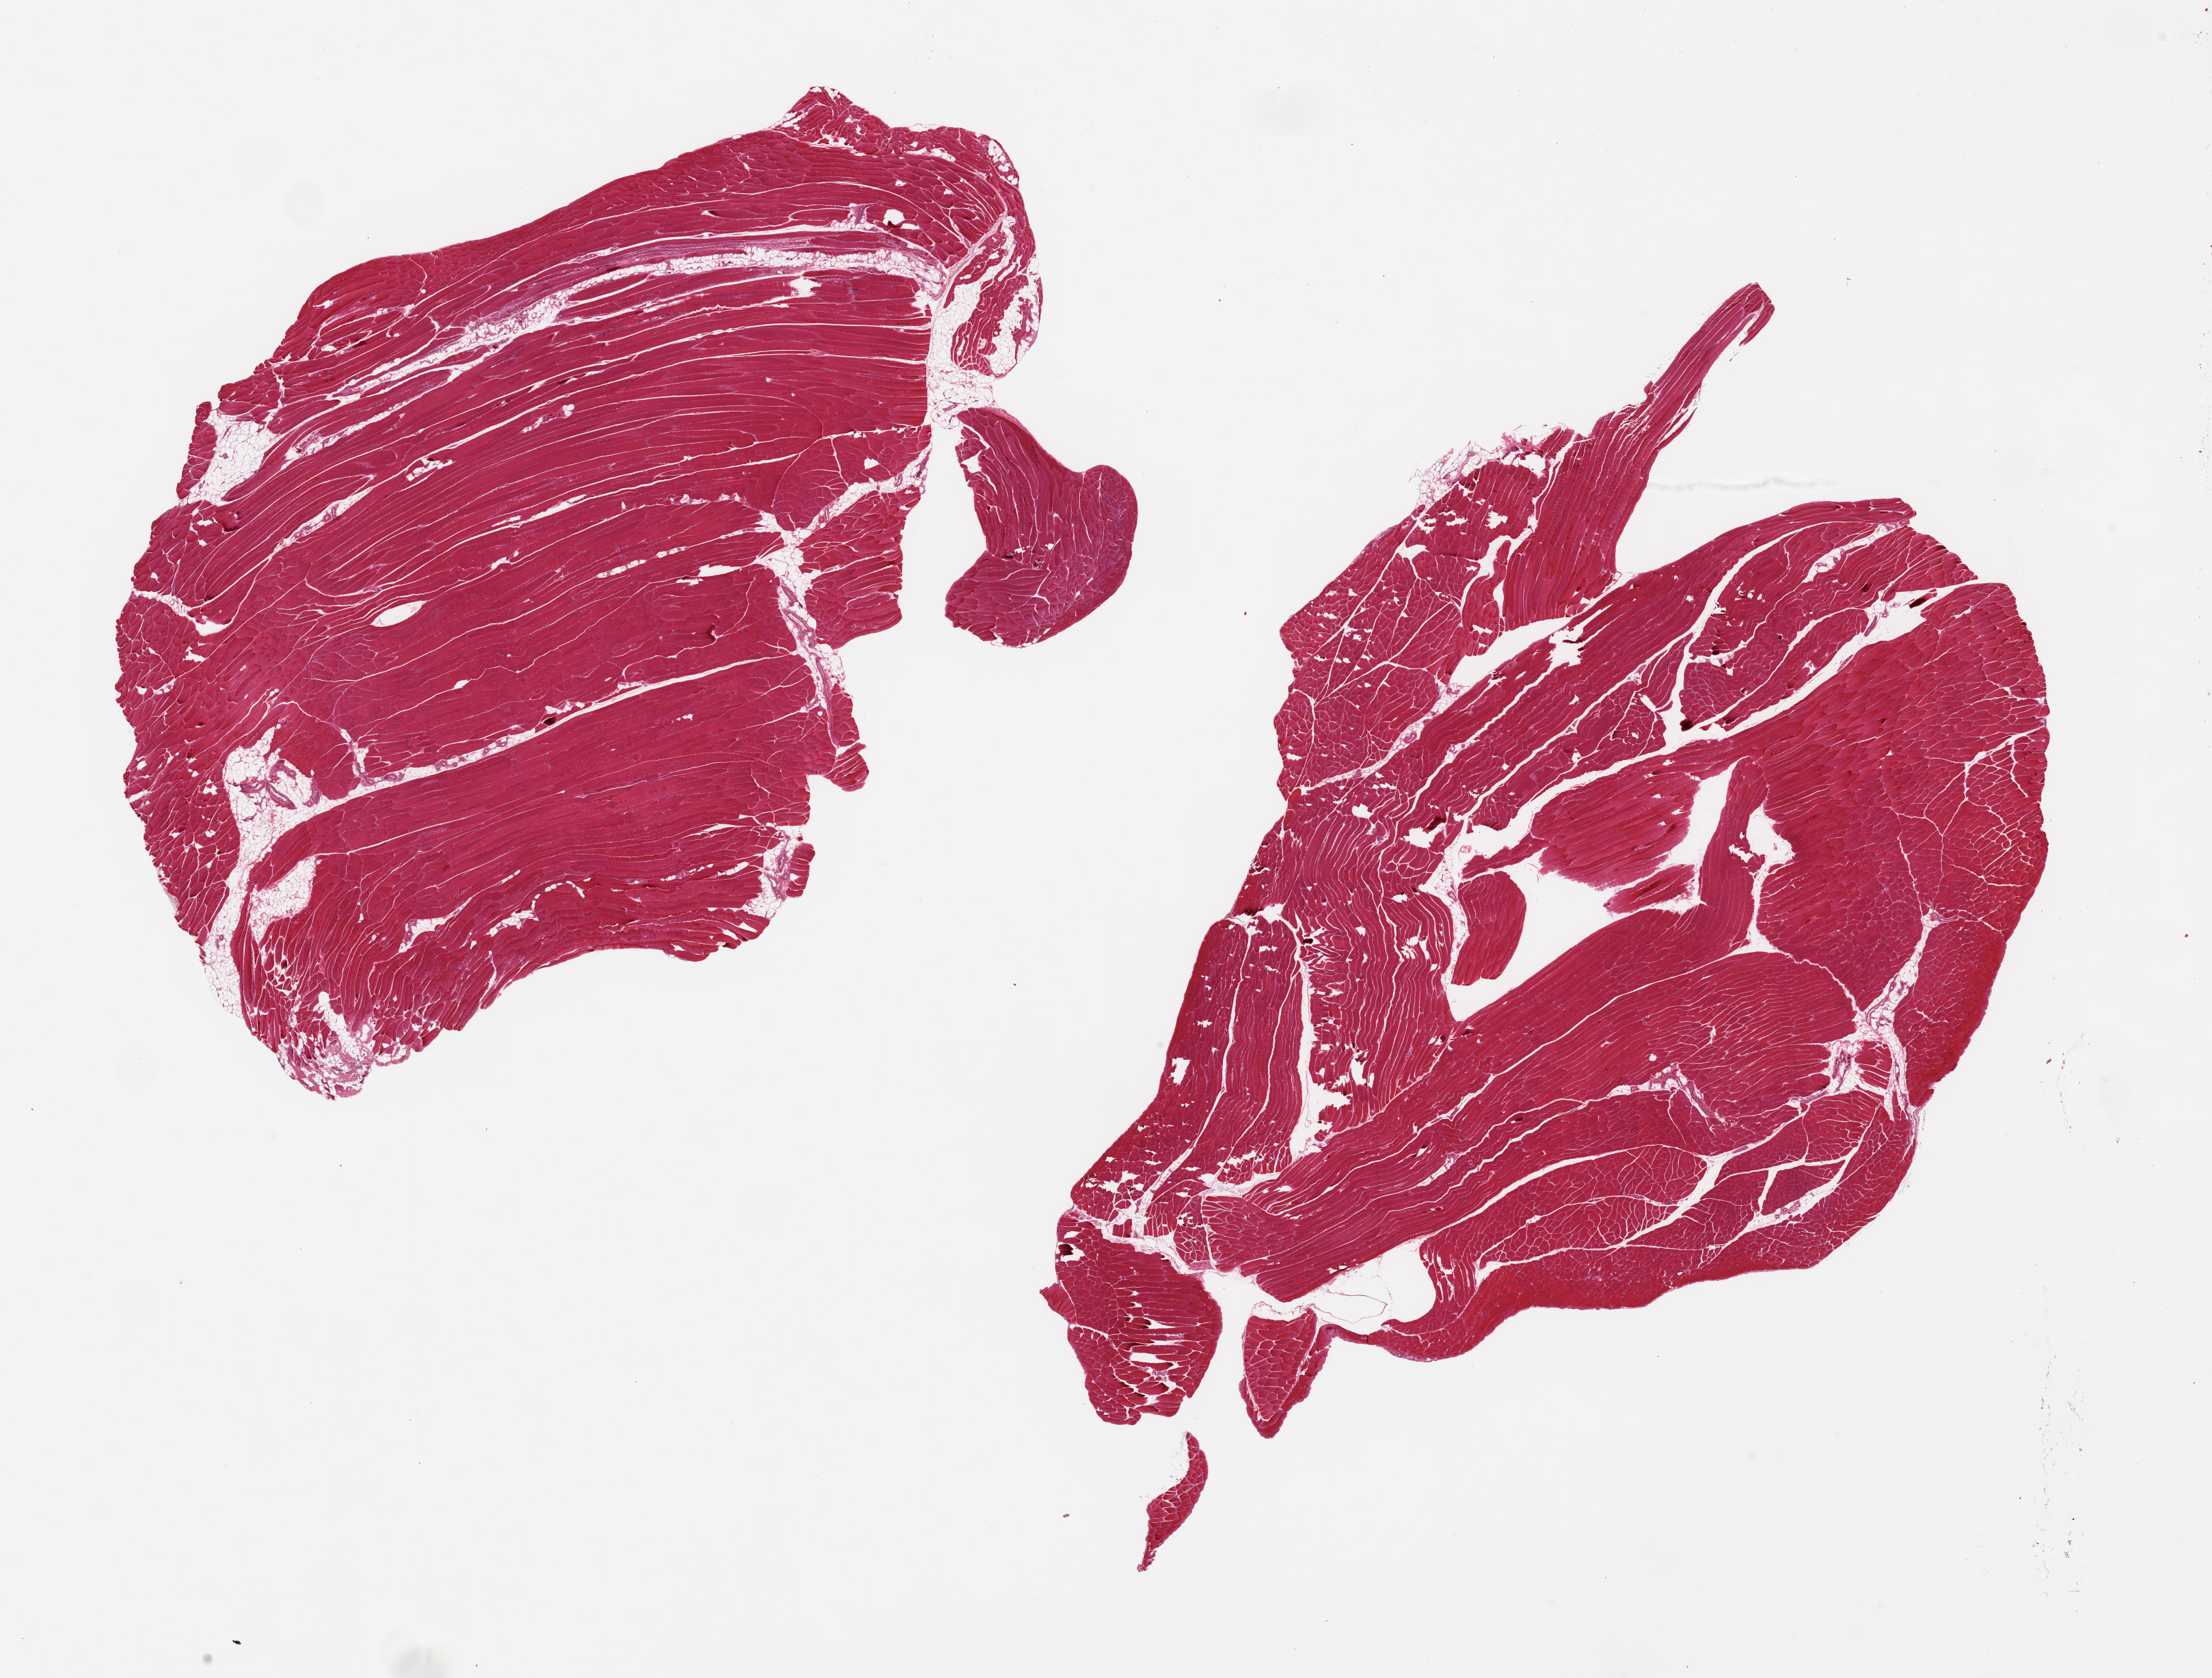
Whole-slide image, hematoxylin and eosin (H&E) stain, brightfield — low-resolution overview of the scanned area, about 25.6 x 19.4 mm. PAXgene-fixed, paraffin-embedded tissue. Target tissue: skeletal muscle. Donor tissue sample.
Review note (as recorded): 2 pieces, ~10% interstitial fat.